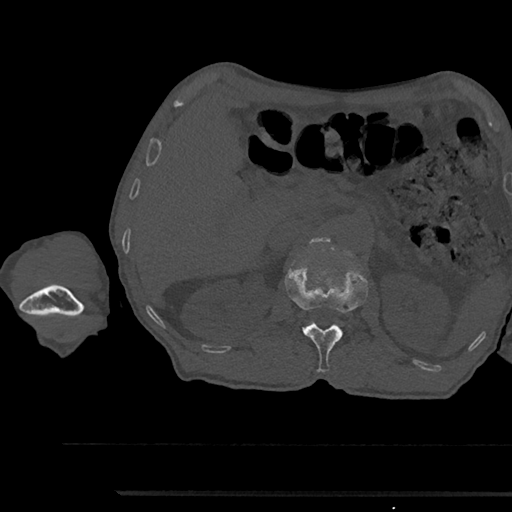
CT including the spine, one axial slice; position 626 of 797 along the scan axis; 120 kVp; bone window (W 1800 / L 400 HU); 512 × 512 image matrix, field of view 367 × 367 mm. Male patient, age 79 years. Case-level facts recorded for this patient, not image findings: primary cancer: prostate.
Annotated regions visible in this slice (semi-automatic segmentation, software-assisted and operator-edited):
- L1 vertebra: bounding box [x1, y1, x2, y2] px = [285, 265, 368, 372]
- L2 vertebra: [310, 237, 328, 243]